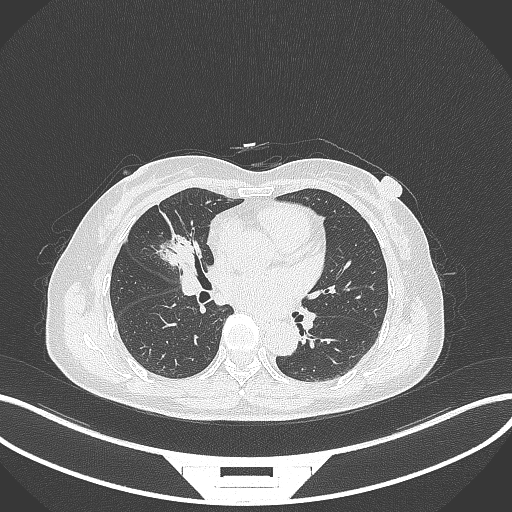
Chest CT, one axial slice; reconstruction kernel B70f; lung window (W 1500 / L -600 HU); 1 mm slice thickness; 512 × 512 image matrix. Patient: female, 51 years. Case-level facts recorded for this patient, not image findings: clinical TNM (as recorded): T1c N0 M0.
Annotated regions visible in this slice (bounding box drawn by a radiologist):
- lung tumour (recorded histology: adenocarcinoma): box from (x=158, y=232) to (x=202, y=271) px